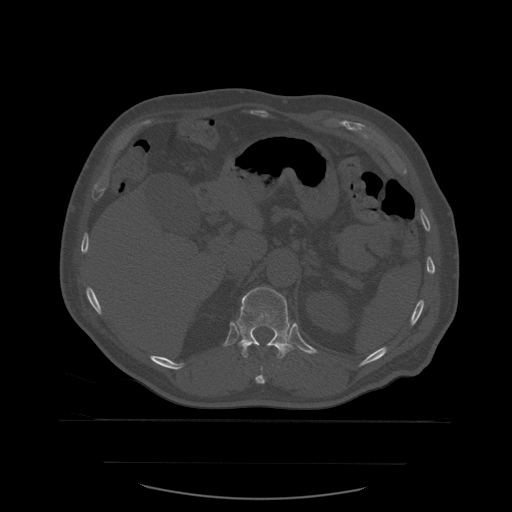
CT including the spine, one axial slice; slice 277 of 590 in the series (ordered by position); bone window (W 1800 / L 400 HU); 1.25 mm slice thickness; 512 × 512 image matrix, field of view 479 × 479 mm. Patient age 71 years. Case-level facts recorded for this patient, not image findings: primary cancer: lung.
Outlined on this slice (semi-automatically segmented with operator editing):
- T11 vertebra: box from (x=256, y=366) to (x=266, y=384) px
- T12 vertebra: (x=235, y=287)–(x=294, y=359)